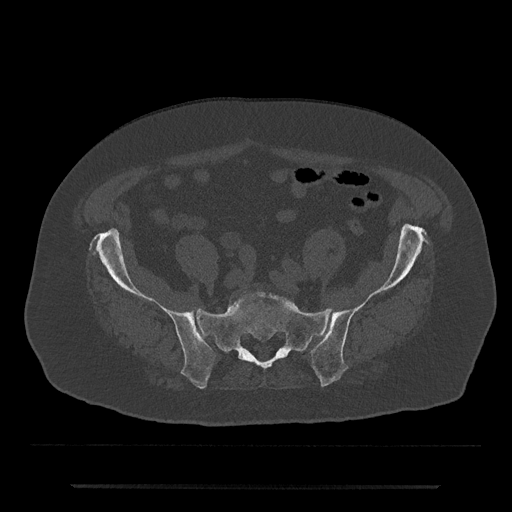
CT including the spine, one axial slice. Slice 233 of 797 in the series (ordered by position). Reconstruction kernel Br40s/3. Bone window (W 1800 / L 400 HU). 0.5 mm slice thickness. 512 × 512 image matrix, field of view 434 × 434 mm. Patient: male, 80 years. From the clinical record (not read from this slice): primary cancer: prostate.
Structures marked on this image (semi-automatically segmented with operator editing):
- L5 vertebra: bounding box [x1, y1, x2, y2] px = [235, 292, 287, 304]